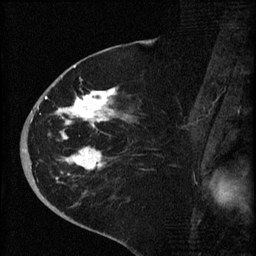
Breast MRI (dynamic contrast-enhanced), one sagittal slice. Position 33 of 60 along the scan axis. Dynamic contrast-enhanced series, image 2 of 4 at this slice position (ordered by acquisition). 1.5 T. TE 4.2 ms, TR 8.2 ms. 2 mm slice thickness. 256 × 256 image matrix, field of view 180 × 180 mm. Patient: female, 71 years.
Annotated regions visible in this slice (semi-automatic segmentation, software-assisted and operator-edited):
- analysis volume of interest (the breast-tissue region the enhancement analysis was run in; not a lesion): bounding box [x1, y1, x2, y2] px = [35, 75, 143, 190]
- tumour enhancement mask (voxels above the 70 % enhancement threshold inside the analysis volume of interest): [37, 87, 127, 180]